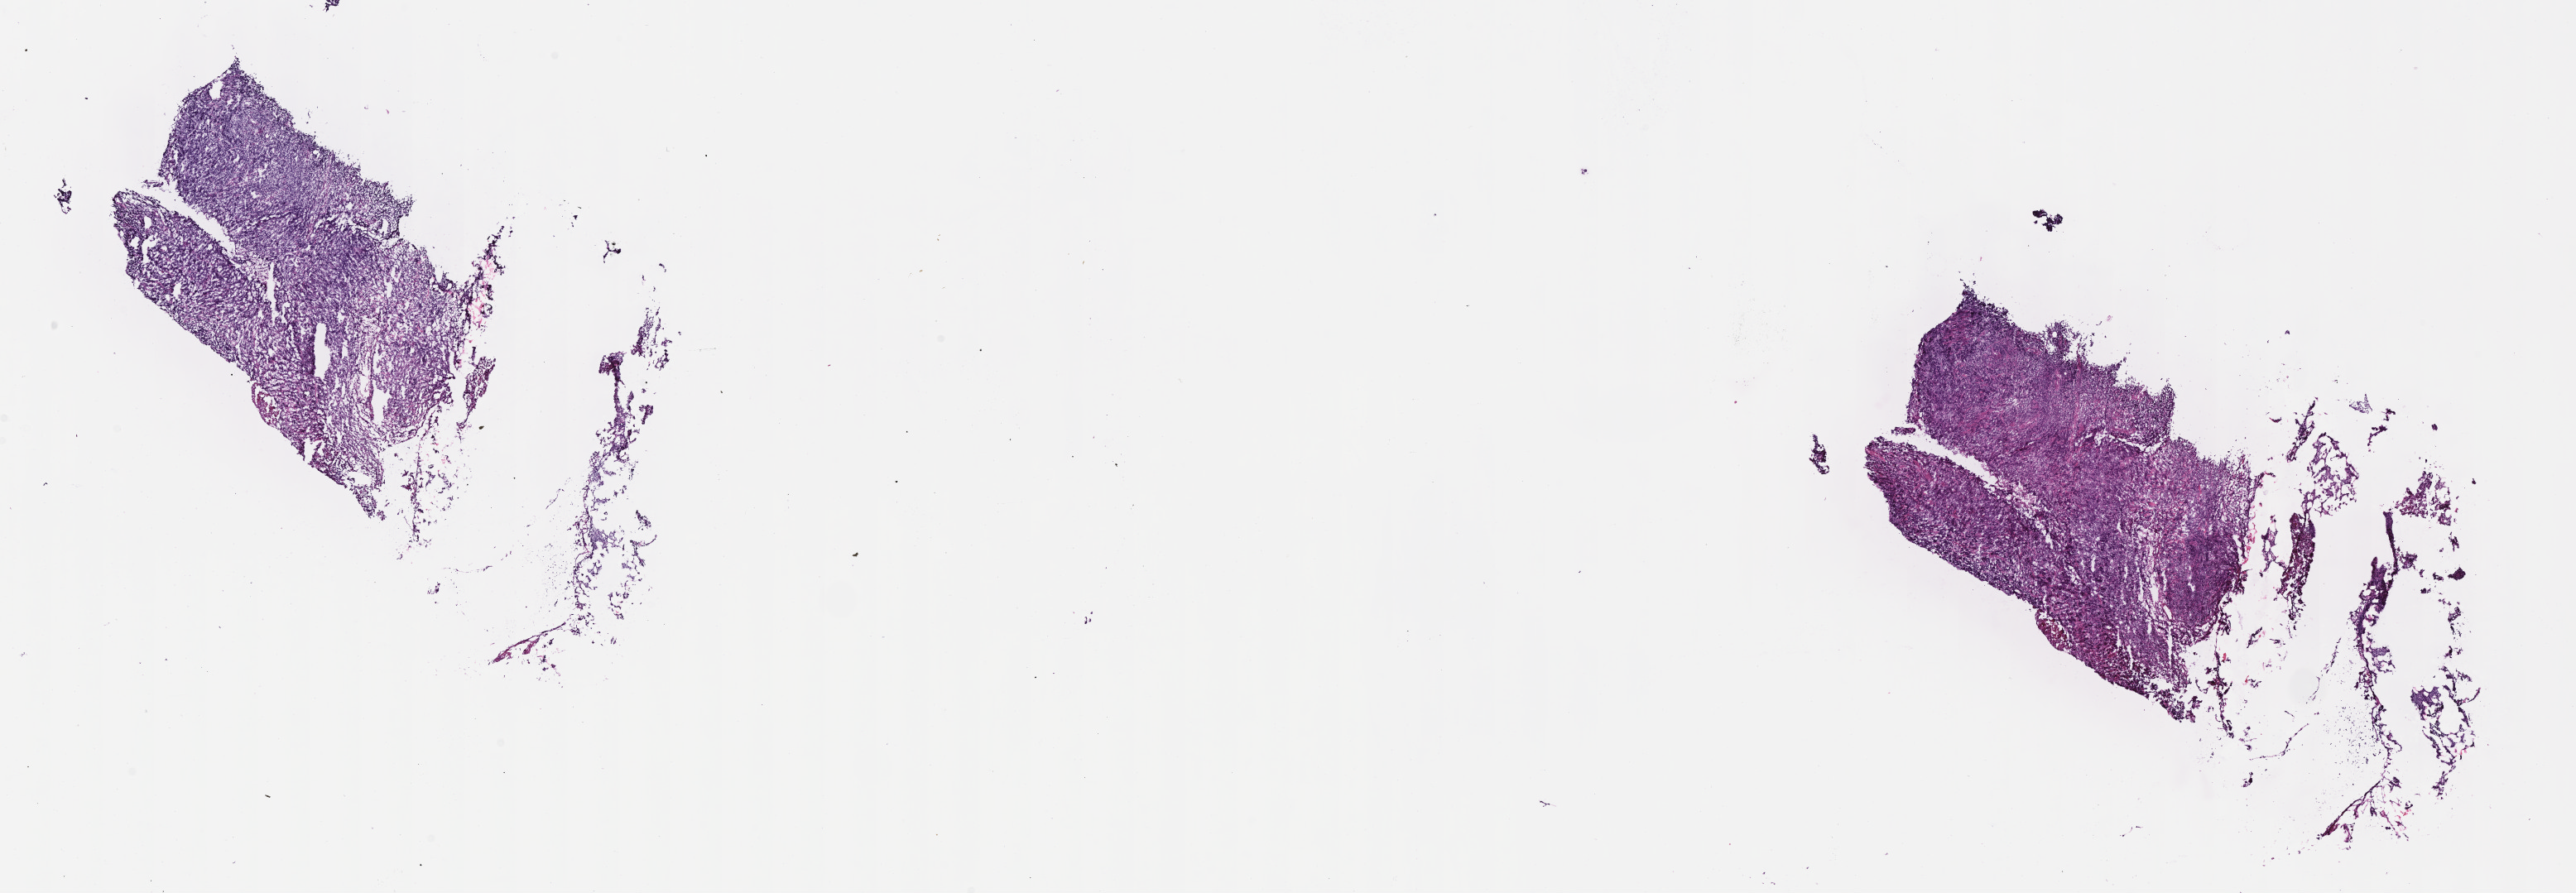
Whole-slide image, haematoxylin and eosin stain, low-resolution overview of the scanned area, about 25.2 x 8.7 mm. Cryosection. Primary tumor. Anatomic site: abdominal lymph node. Patient: male, age at initial diagnosis 9 years. Pathologist review of this section (percent, as recorded): tumor cells 95%, tumor nuclei 95%, stromal cells 3%, necrosis 2%, normal cells 0%. Infiltration values recorded for this section: lymphocyte infiltration 2%, monocyte infiltration 2%, neutrophil infiltration 0%.
- Ann Arbor stage (patient): Stage III
- histologic diagnosis: Burkitt lymphoma, NOS
- section: top of the tissue portion